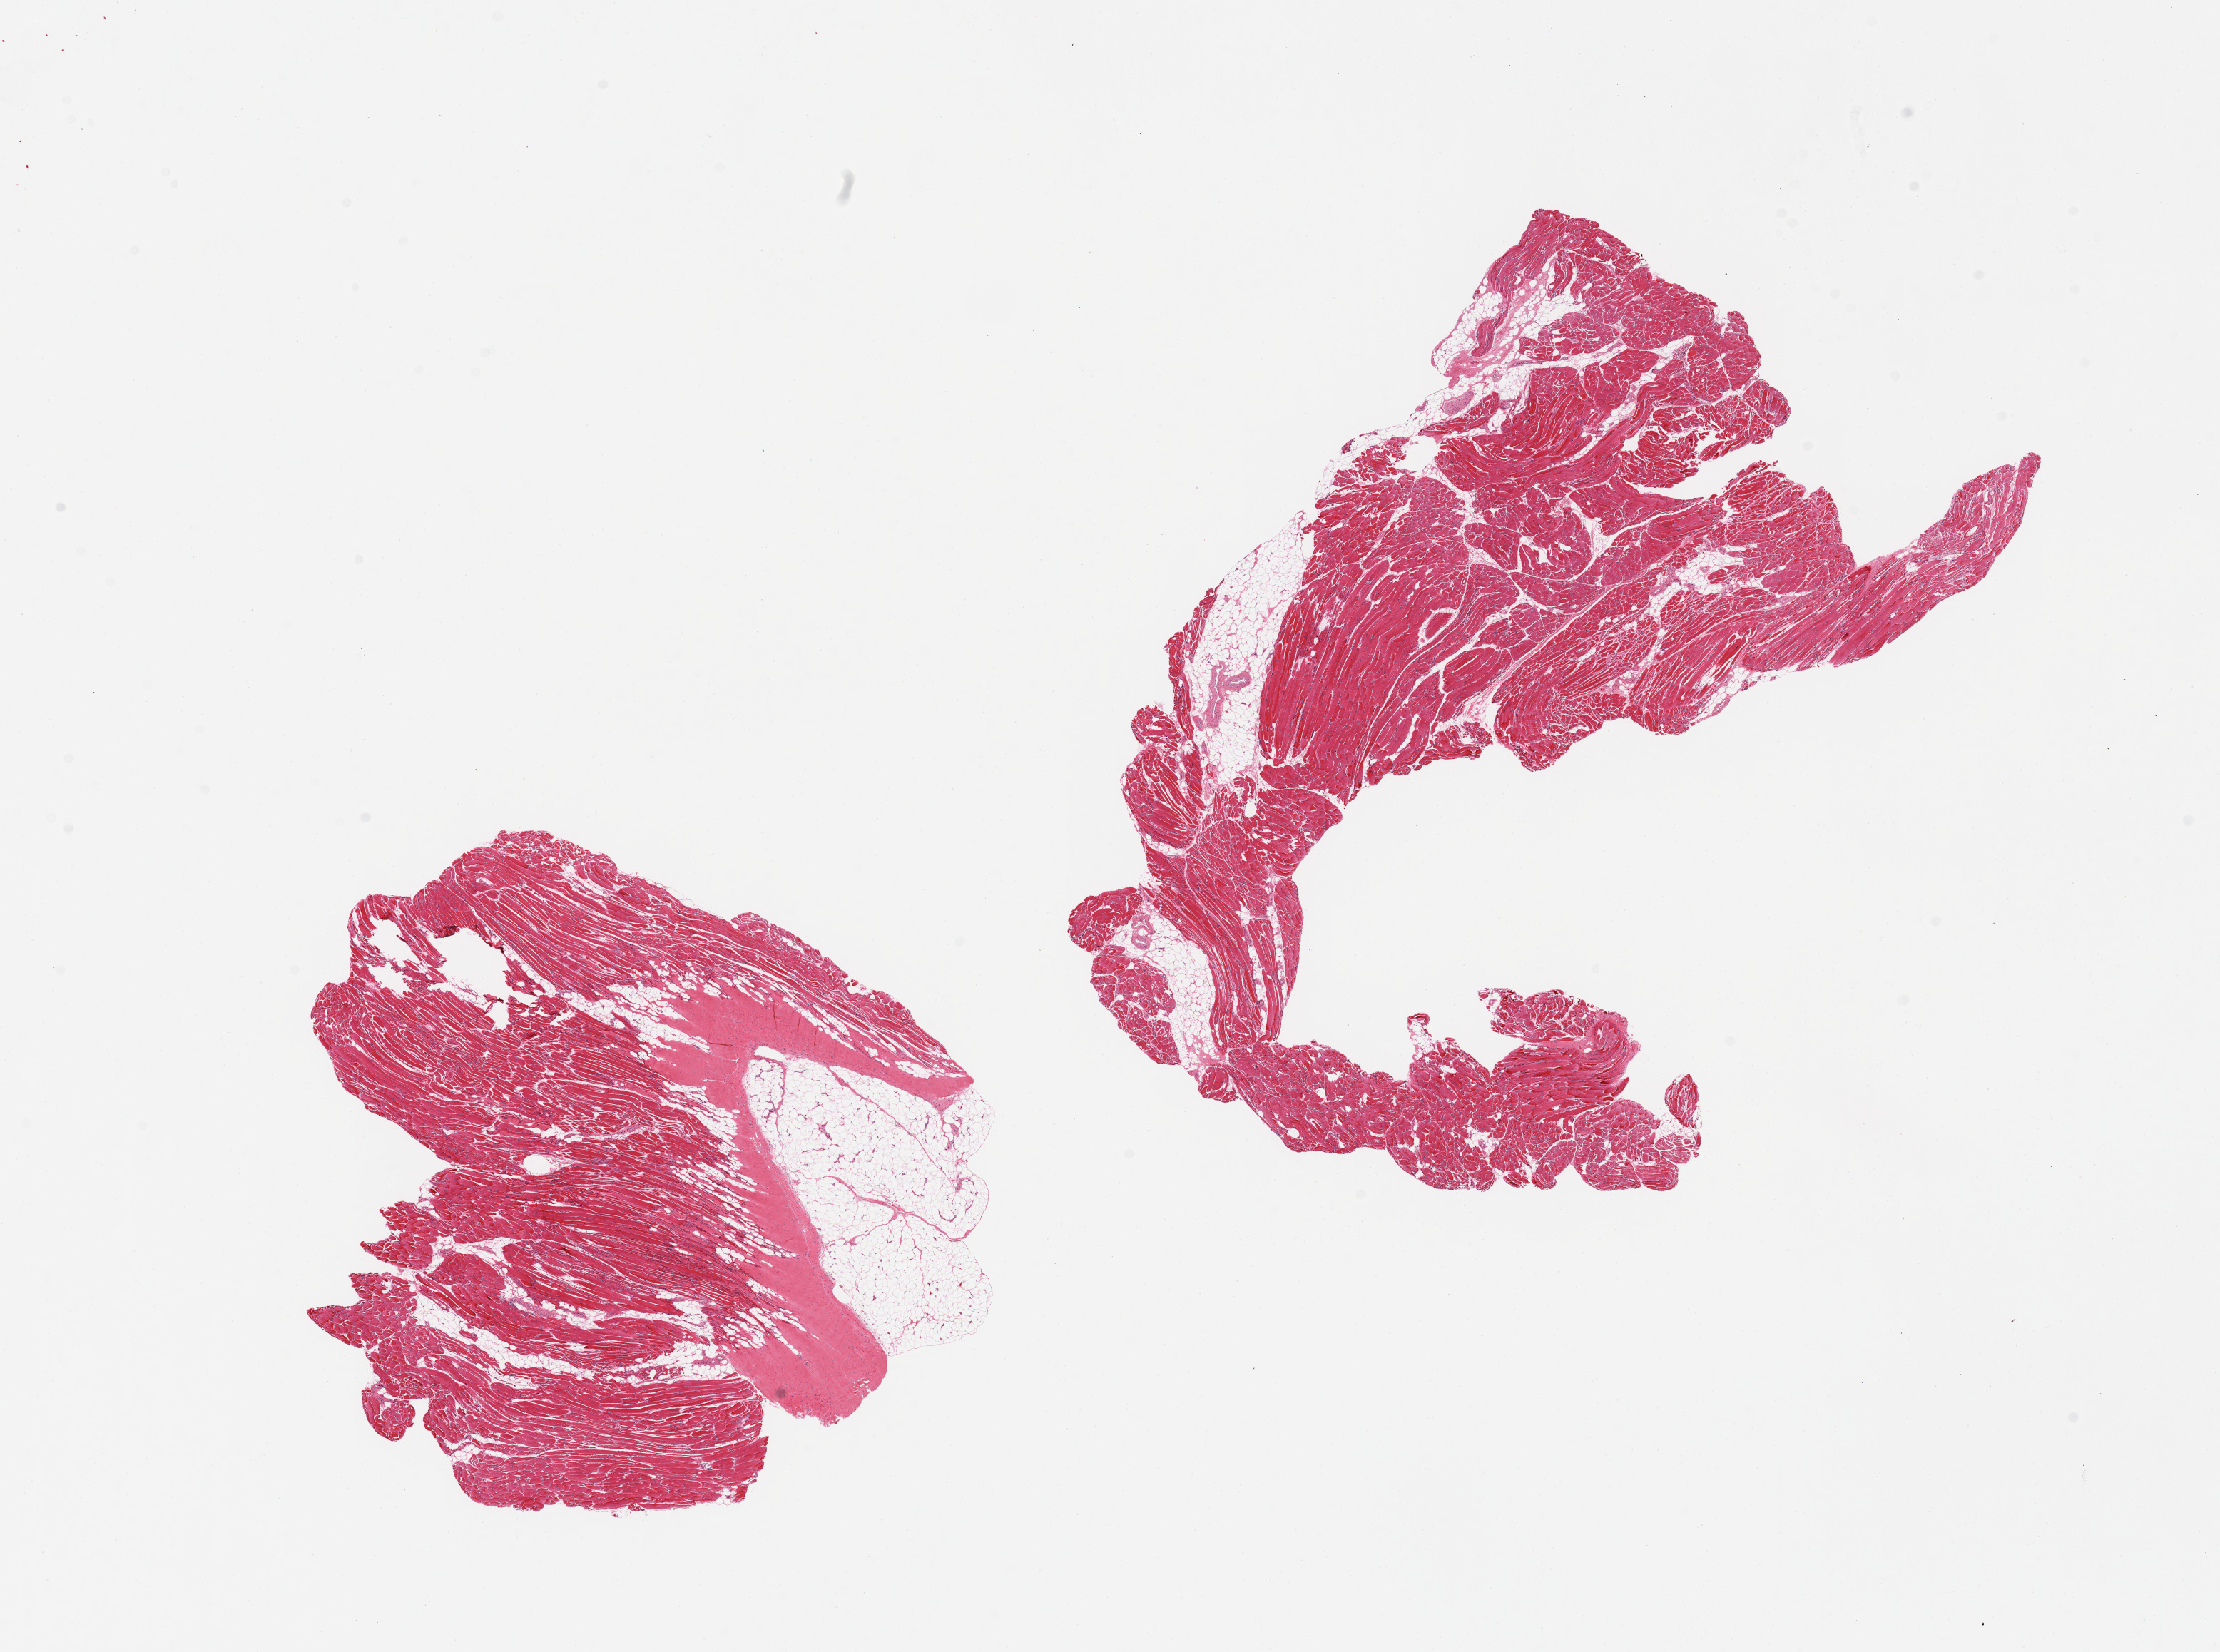
Digitized haematoxylin and eosin-stained section, a low-resolution overview of the entire scanned area, about 24.6 x 18.3 mm (slide scanned at 20x), PAXgene-fixed paraffin-embedded (PFPE) section, section of skeletal muscle (target tissue), donor tissue sample. Female donor.
* pathologist's review note for this sample: 2 pieces; 1 with 25% fibroadipose tissue; 1 with 10% fat; scattered atrophic fibers